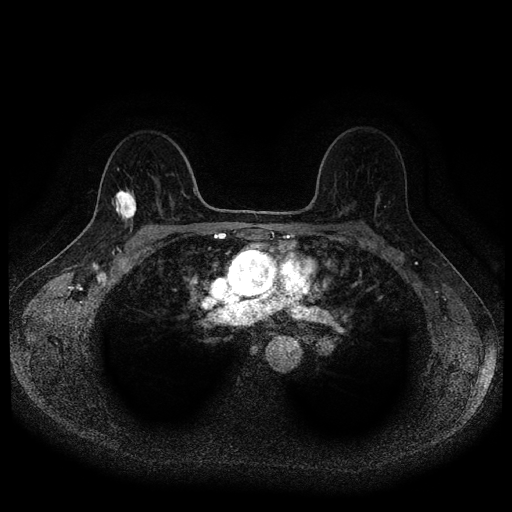
Breast MRI (dynamic contrast-enhanced, multi-phase), one axial slice; position 68 of 116 along the scan axis; dynamic contrast-enhanced series, time point 2 of 5 at this slice position (early post-contrast); 1.5 T; TE 2.6 ms, TR 5.4 ms; 2 mm slice thickness; 512 × 512 image matrix. Female patient, age 49 years.
Annotated regions visible in this slice (semi-automatically segmented with operator editing):
- breast lesion (labelled 'tumour' in the annotation; benign lesions carry a separate 'benign' label): bounding box (x1, y1, x2, y2) in pixels: (111, 186, 137, 224)